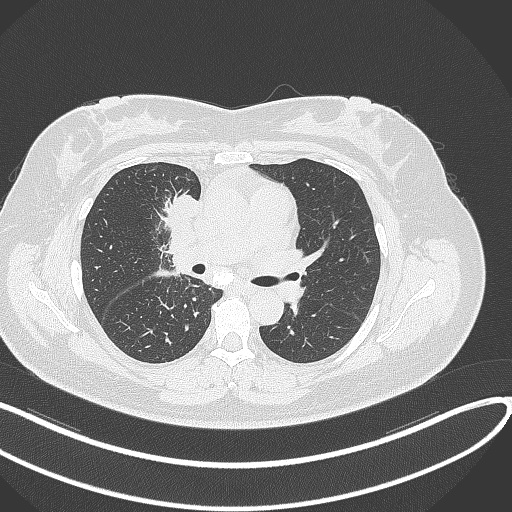
Chest CT, one axial slice. Slice 157 of 303 in the series (ordered by position). 120 kVp. Lung window (W 1500 / L -600 HU). 1 mm slice thickness. 512 × 512 image matrix, field of view 400 × 400 mm. Female patient, age 46 years. Case-level facts recorded for this patient, not image findings: clinical TNM (as recorded): T2a N1 M0.
Outlined on this slice (rectangle marked by the reading radiologist):
- lung tumour (recorded histology: adenocarcinoma): bounding box (x1, y1, x2, y2) in pixels: (171, 192, 199, 222)